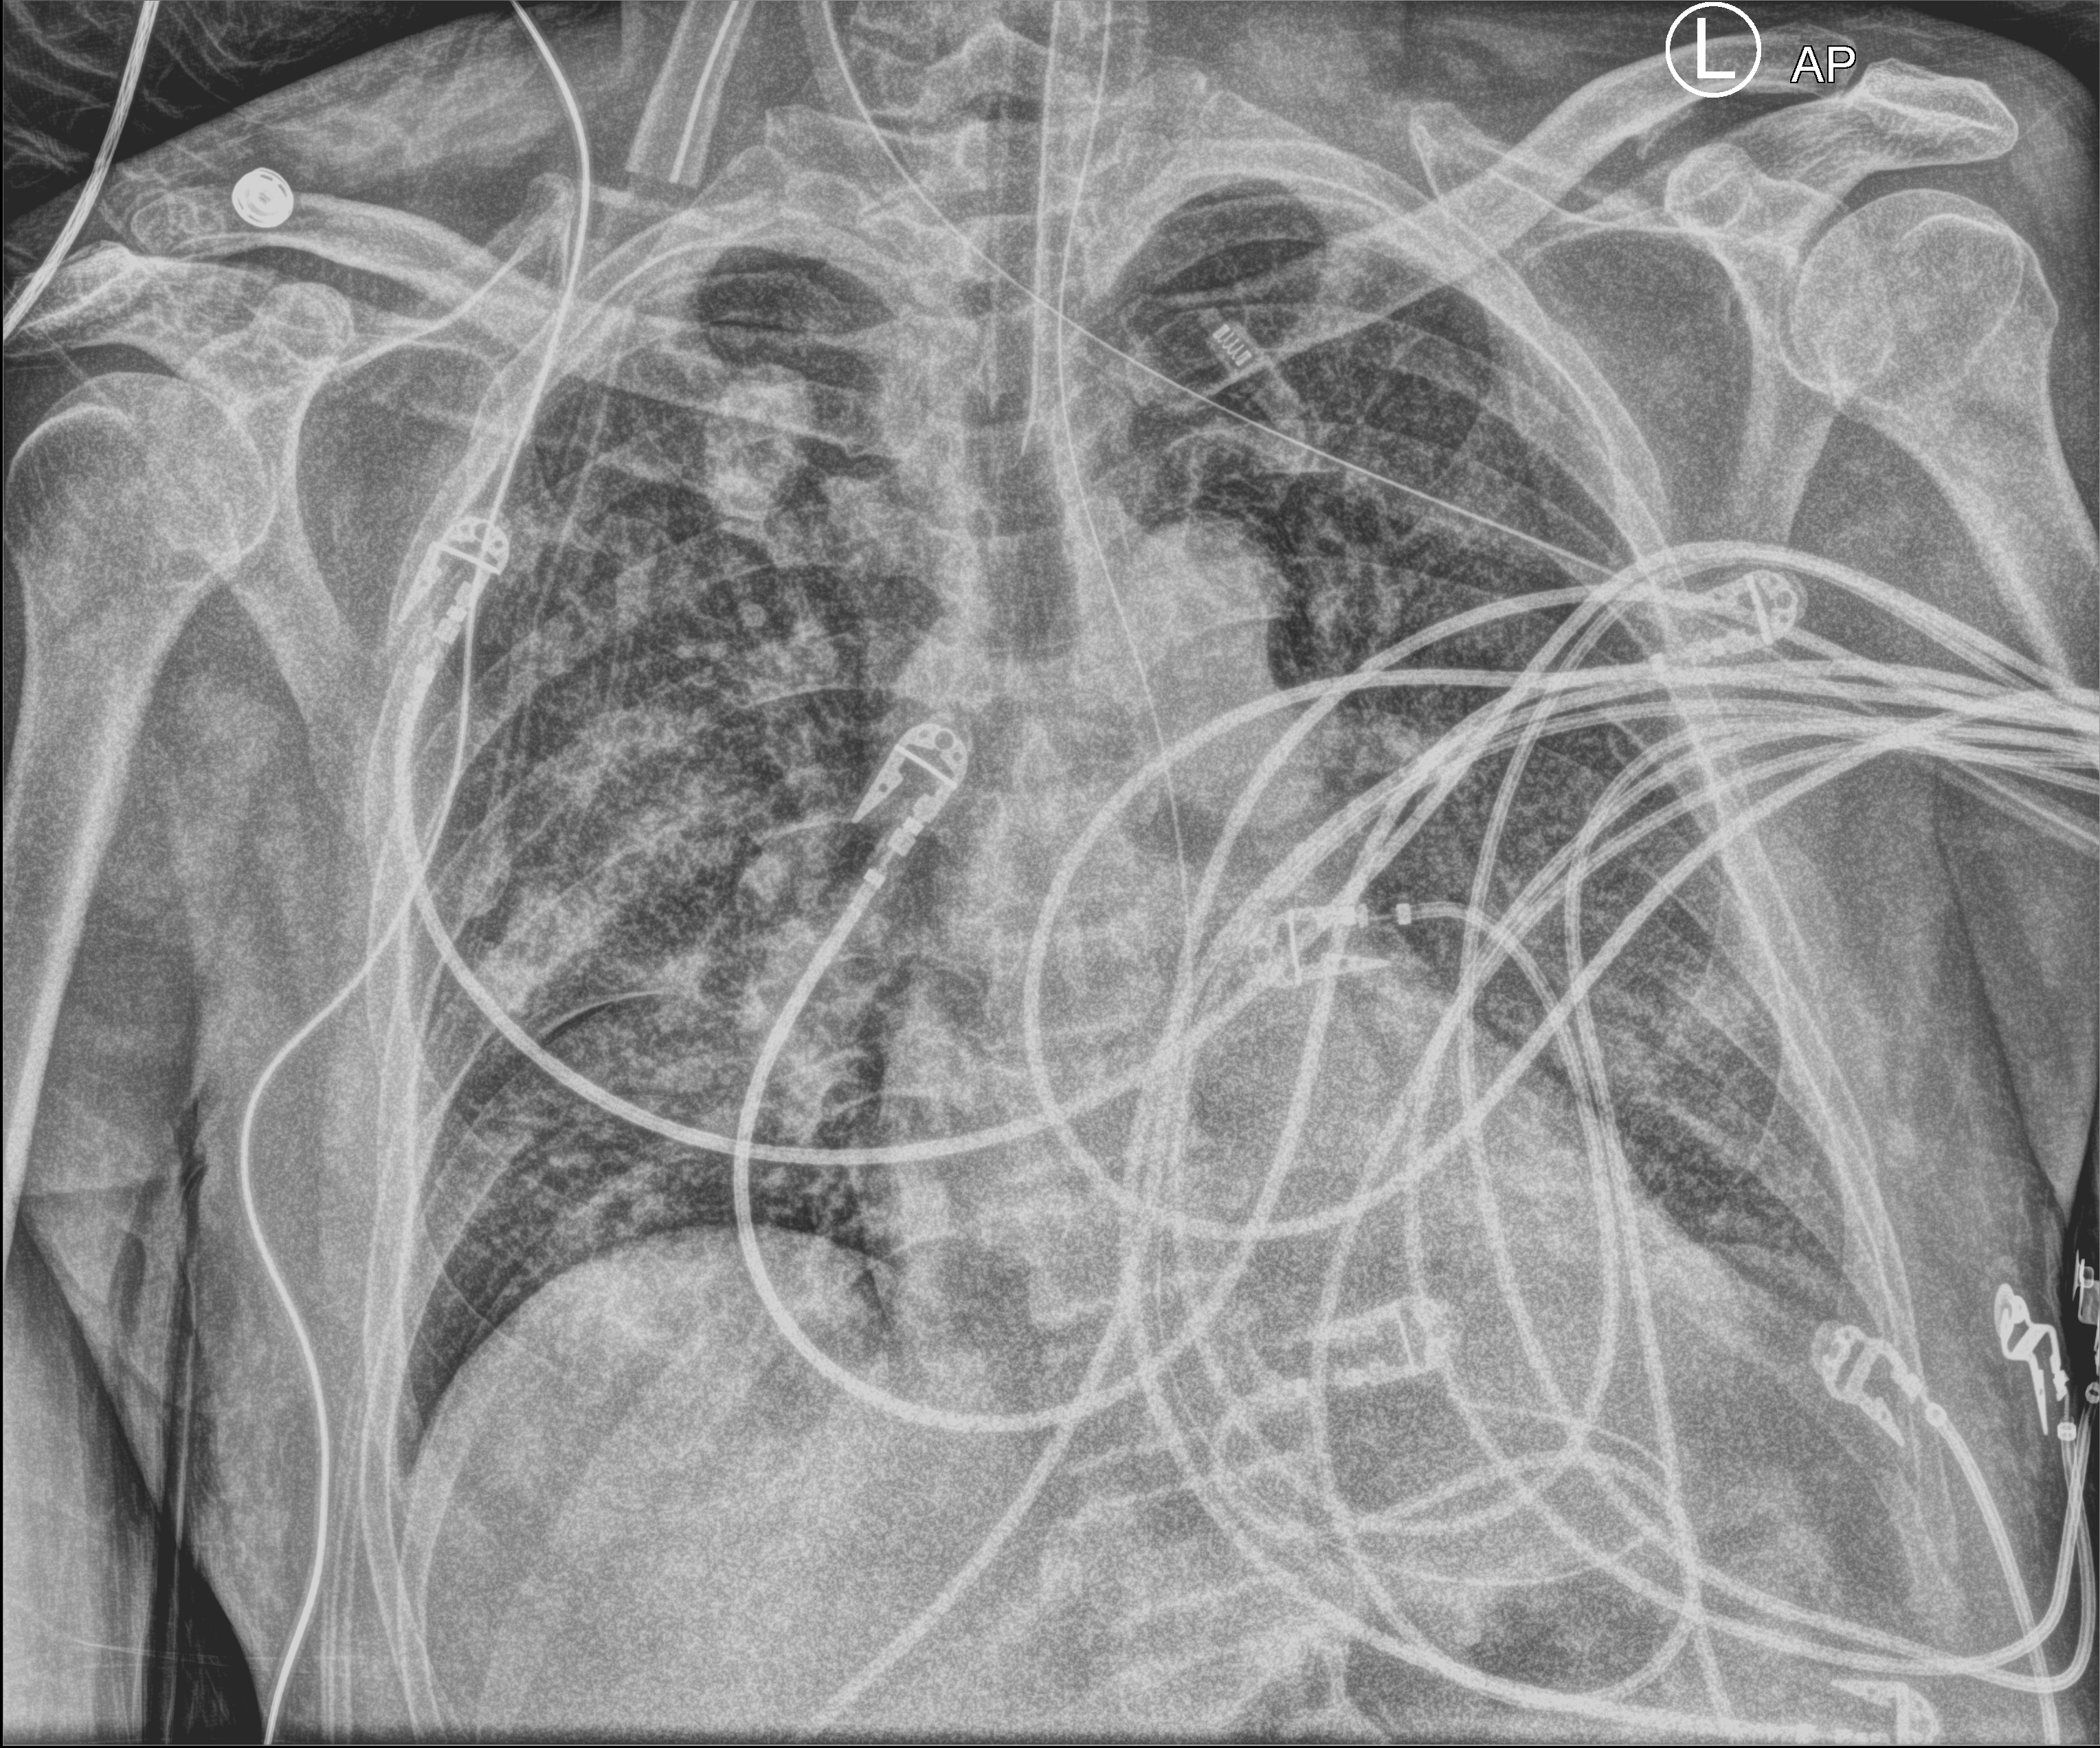
Bedside chest radiograph (computed radiography), anteroposterior (AP) projection. Patient hospitalised with COVID-19; male, aged 60–74 years.
Admission-level facts for this patient (not findings on this image; timing relative to this image not recorded): smoking status (admission record): former; mechanically ventilated during this hospital stay: yes.